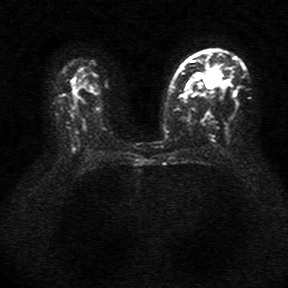
Breast MRI, one axial slice; slice 22 of 34 in the series (ordered by position); diffusion-weighted series; image 2 of 4 stored at this slice position (different b-values; order by instance number); 1.5 T; 5 mm slice thickness; 288 × 288 image matrix, field of view 340 × 340 mm. Female patient.
Outlined on this slice (manually delineated by an expert):
- tumour on diffusion-weighted imaging: box from (x=205, y=71) to (x=219, y=87) px